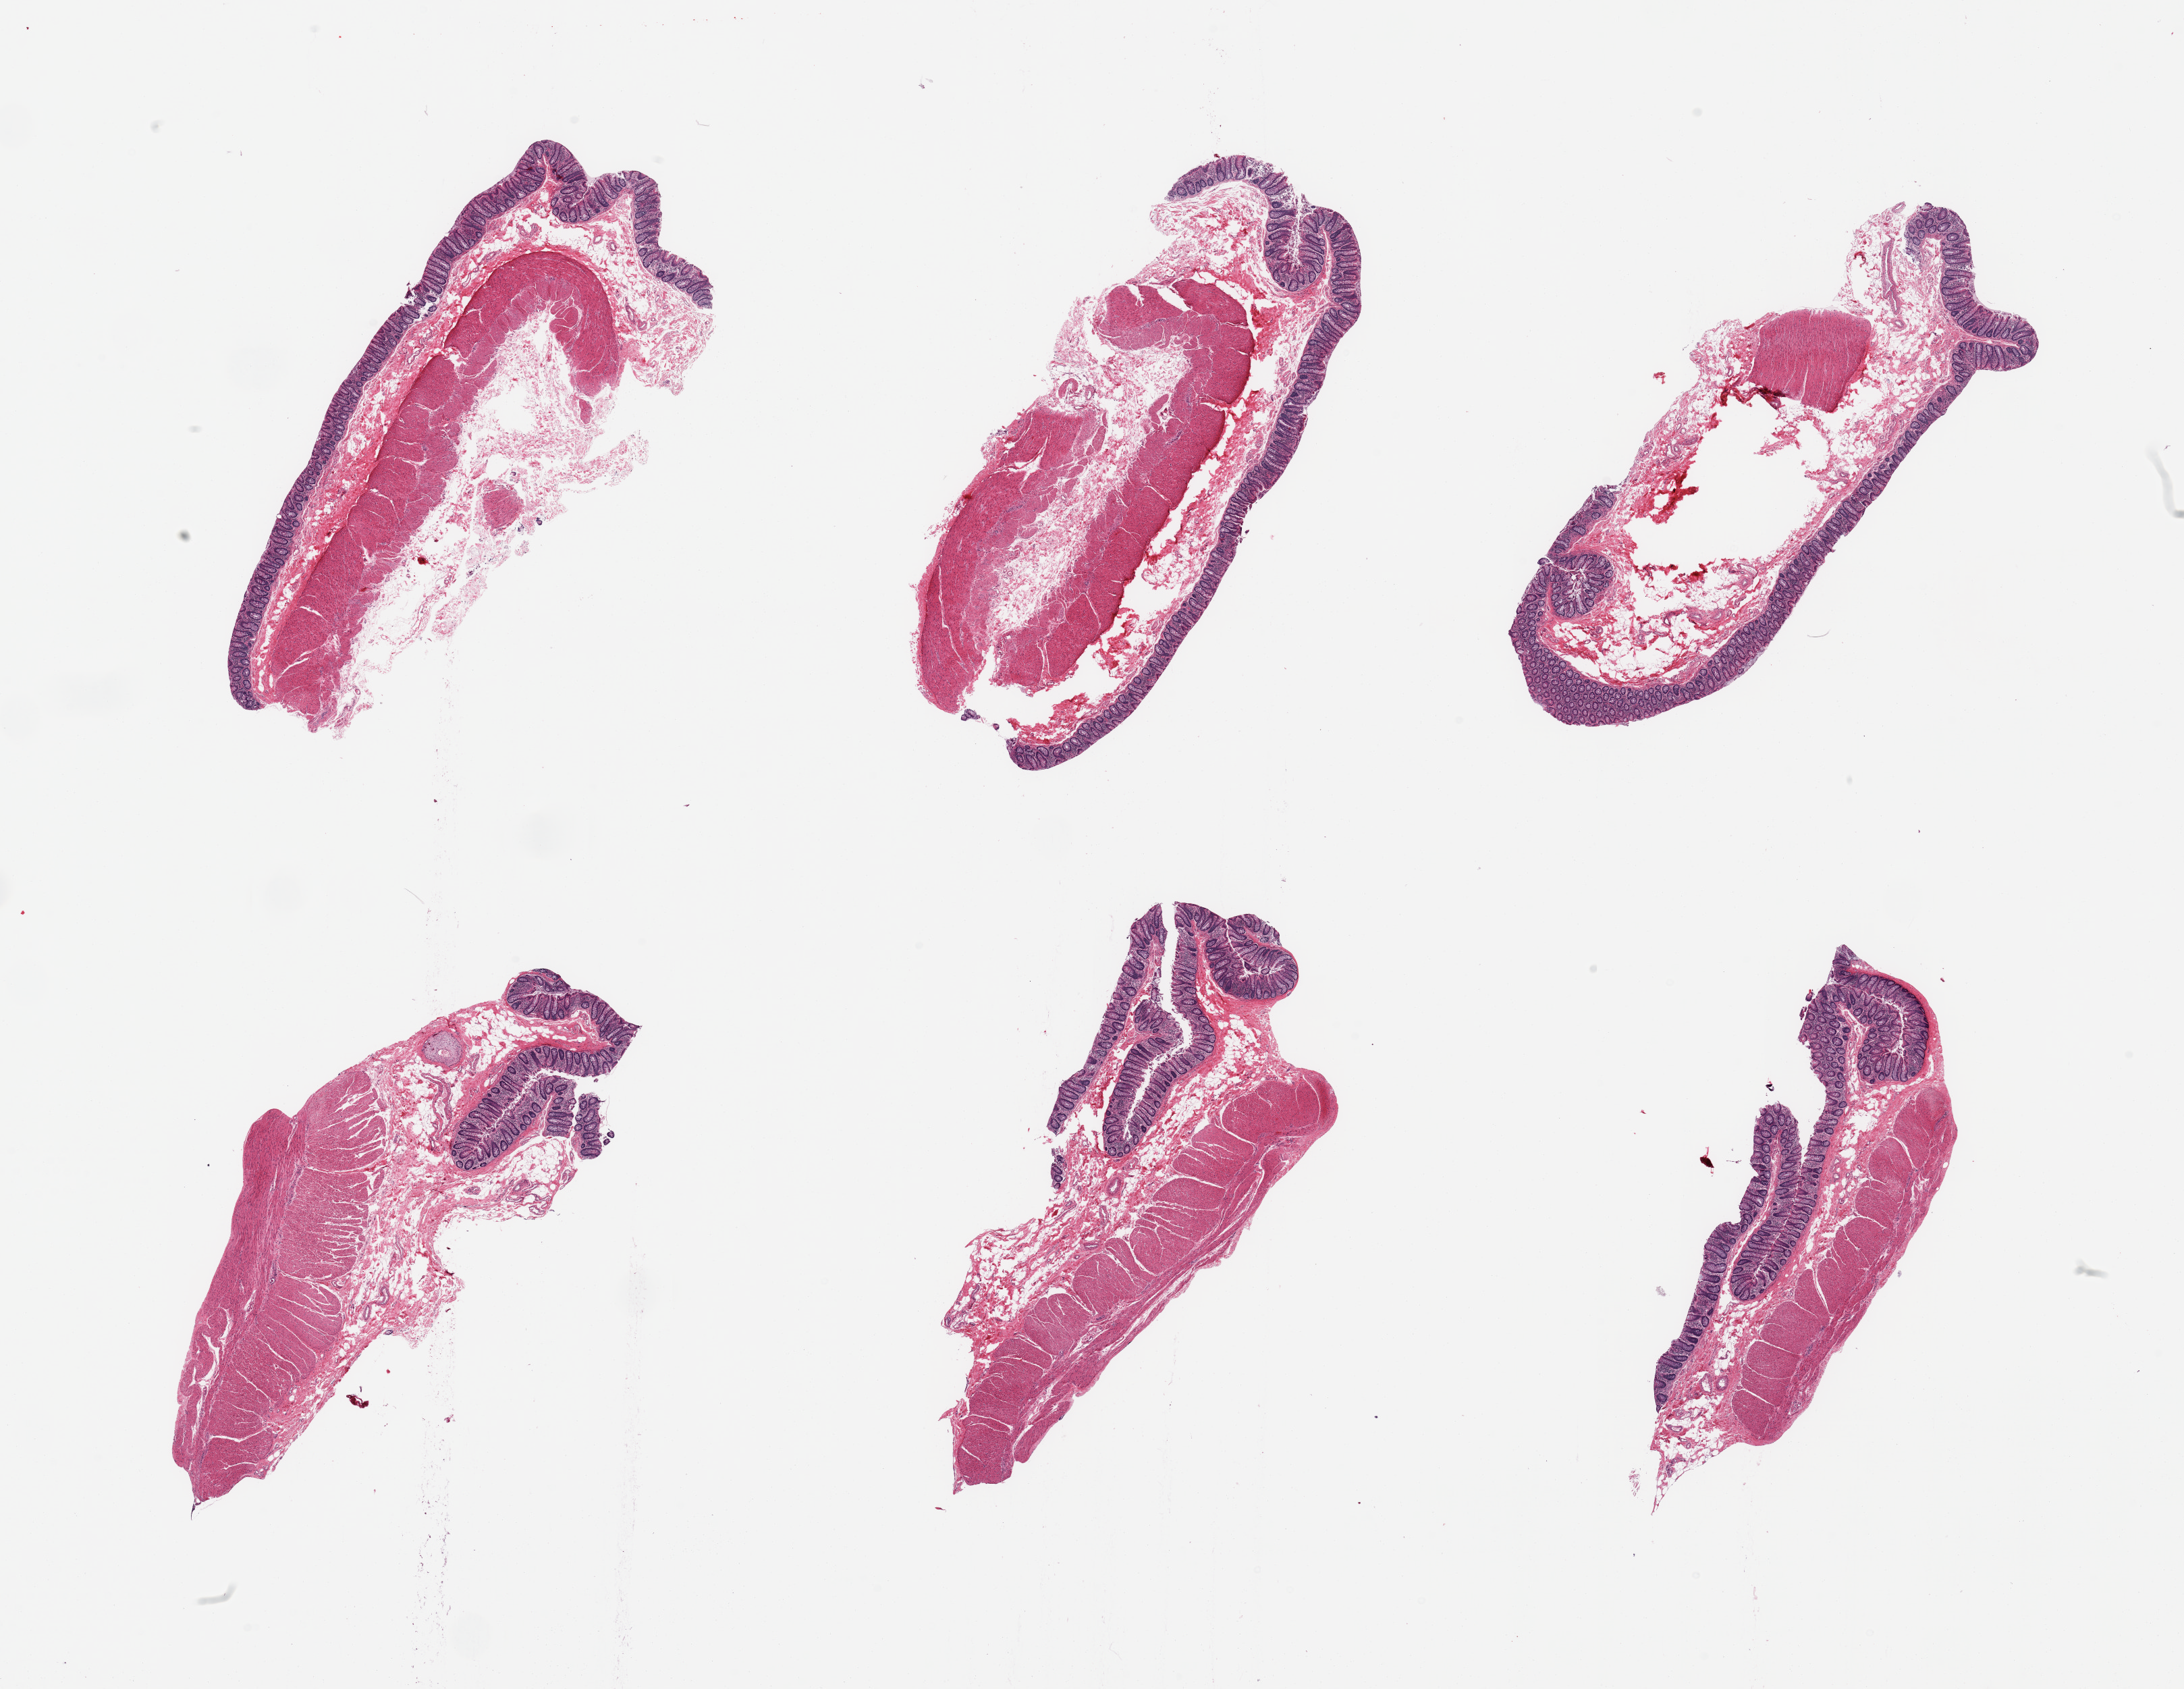
Hematoxylin and eosin (H&E) whole-slide image, brightfield — a low-resolution overview of the entire scanned area, about 25.6 x 19.8 mm. PAXgene-fixed paraffin-embedded (PFPE) section. Section of transverse colon (target tissue). Tissue donor sample. Donor: male.
Pathologist's review note for this sample: 6 pieces, well preserved mucosa up to ~0.25mm.